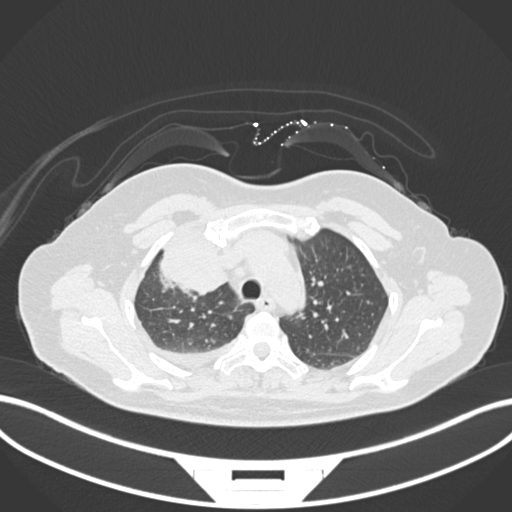
Chest CT, one axial slice; position 123 of 172 along the scan axis; 120 kVp; lung window (W 1500 / L -600 HU); 1 mm slice thickness; 512 × 512 image matrix, field of view 400 × 400 mm. Patient: female, 52 years. From the clinical record (not read from this slice): clinical TNM (as recorded): T3 N1 M1.
Outlined on this slice (rectangle marked by the reading radiologist):
- lung tumour (recorded histology: adenocarcinoma): bounding box <154,222,236,296> (left, top, right, bottom; pixels)